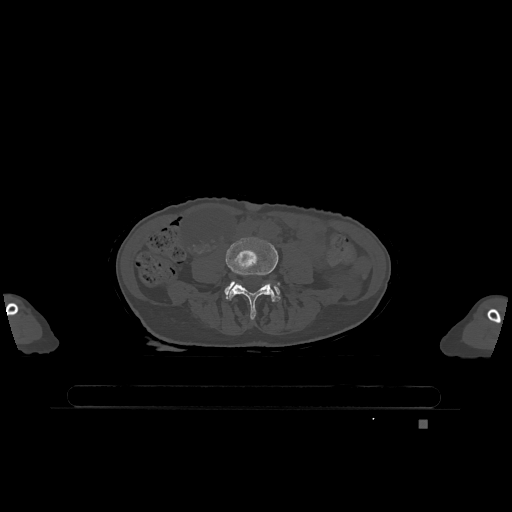
CT including the spine, one axial slice; position 288 of 1317 along the scan axis; bone window (W 1800 / L 400 HU); 0.5 mm slice thickness; 512 × 512 image matrix, field of view 500 × 500 mm. Female patient, age 74 years. Case-level facts recorded for this patient, not image findings: primary cancer: lung.
Outlined on this slice (semi-automatically segmented with operator editing):
- L4 vertebra: box from (x=226, y=236) to (x=280, y=320) px
- L5 vertebra: (x=225, y=281)–(x=280, y=301)